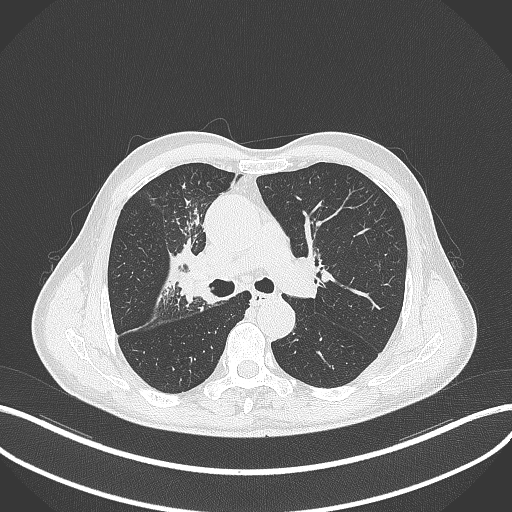
Chest CT, one axial slice; position 306 of 490 along the scan axis; 120 kVp; lung window (W 1500 / L -600 HU); 1 mm slice thickness; 512 × 512 image matrix. Male patient, age 69 years. From the clinical record (not read from this slice): clinical TNM (as recorded): T2a N0 M0.
Outlined on this slice (bounding box drawn by a radiologist):
- lung tumour (recorded histology: adenocarcinoma): bounding box [x1, y1, x2, y2] px = [168, 248, 211, 306]